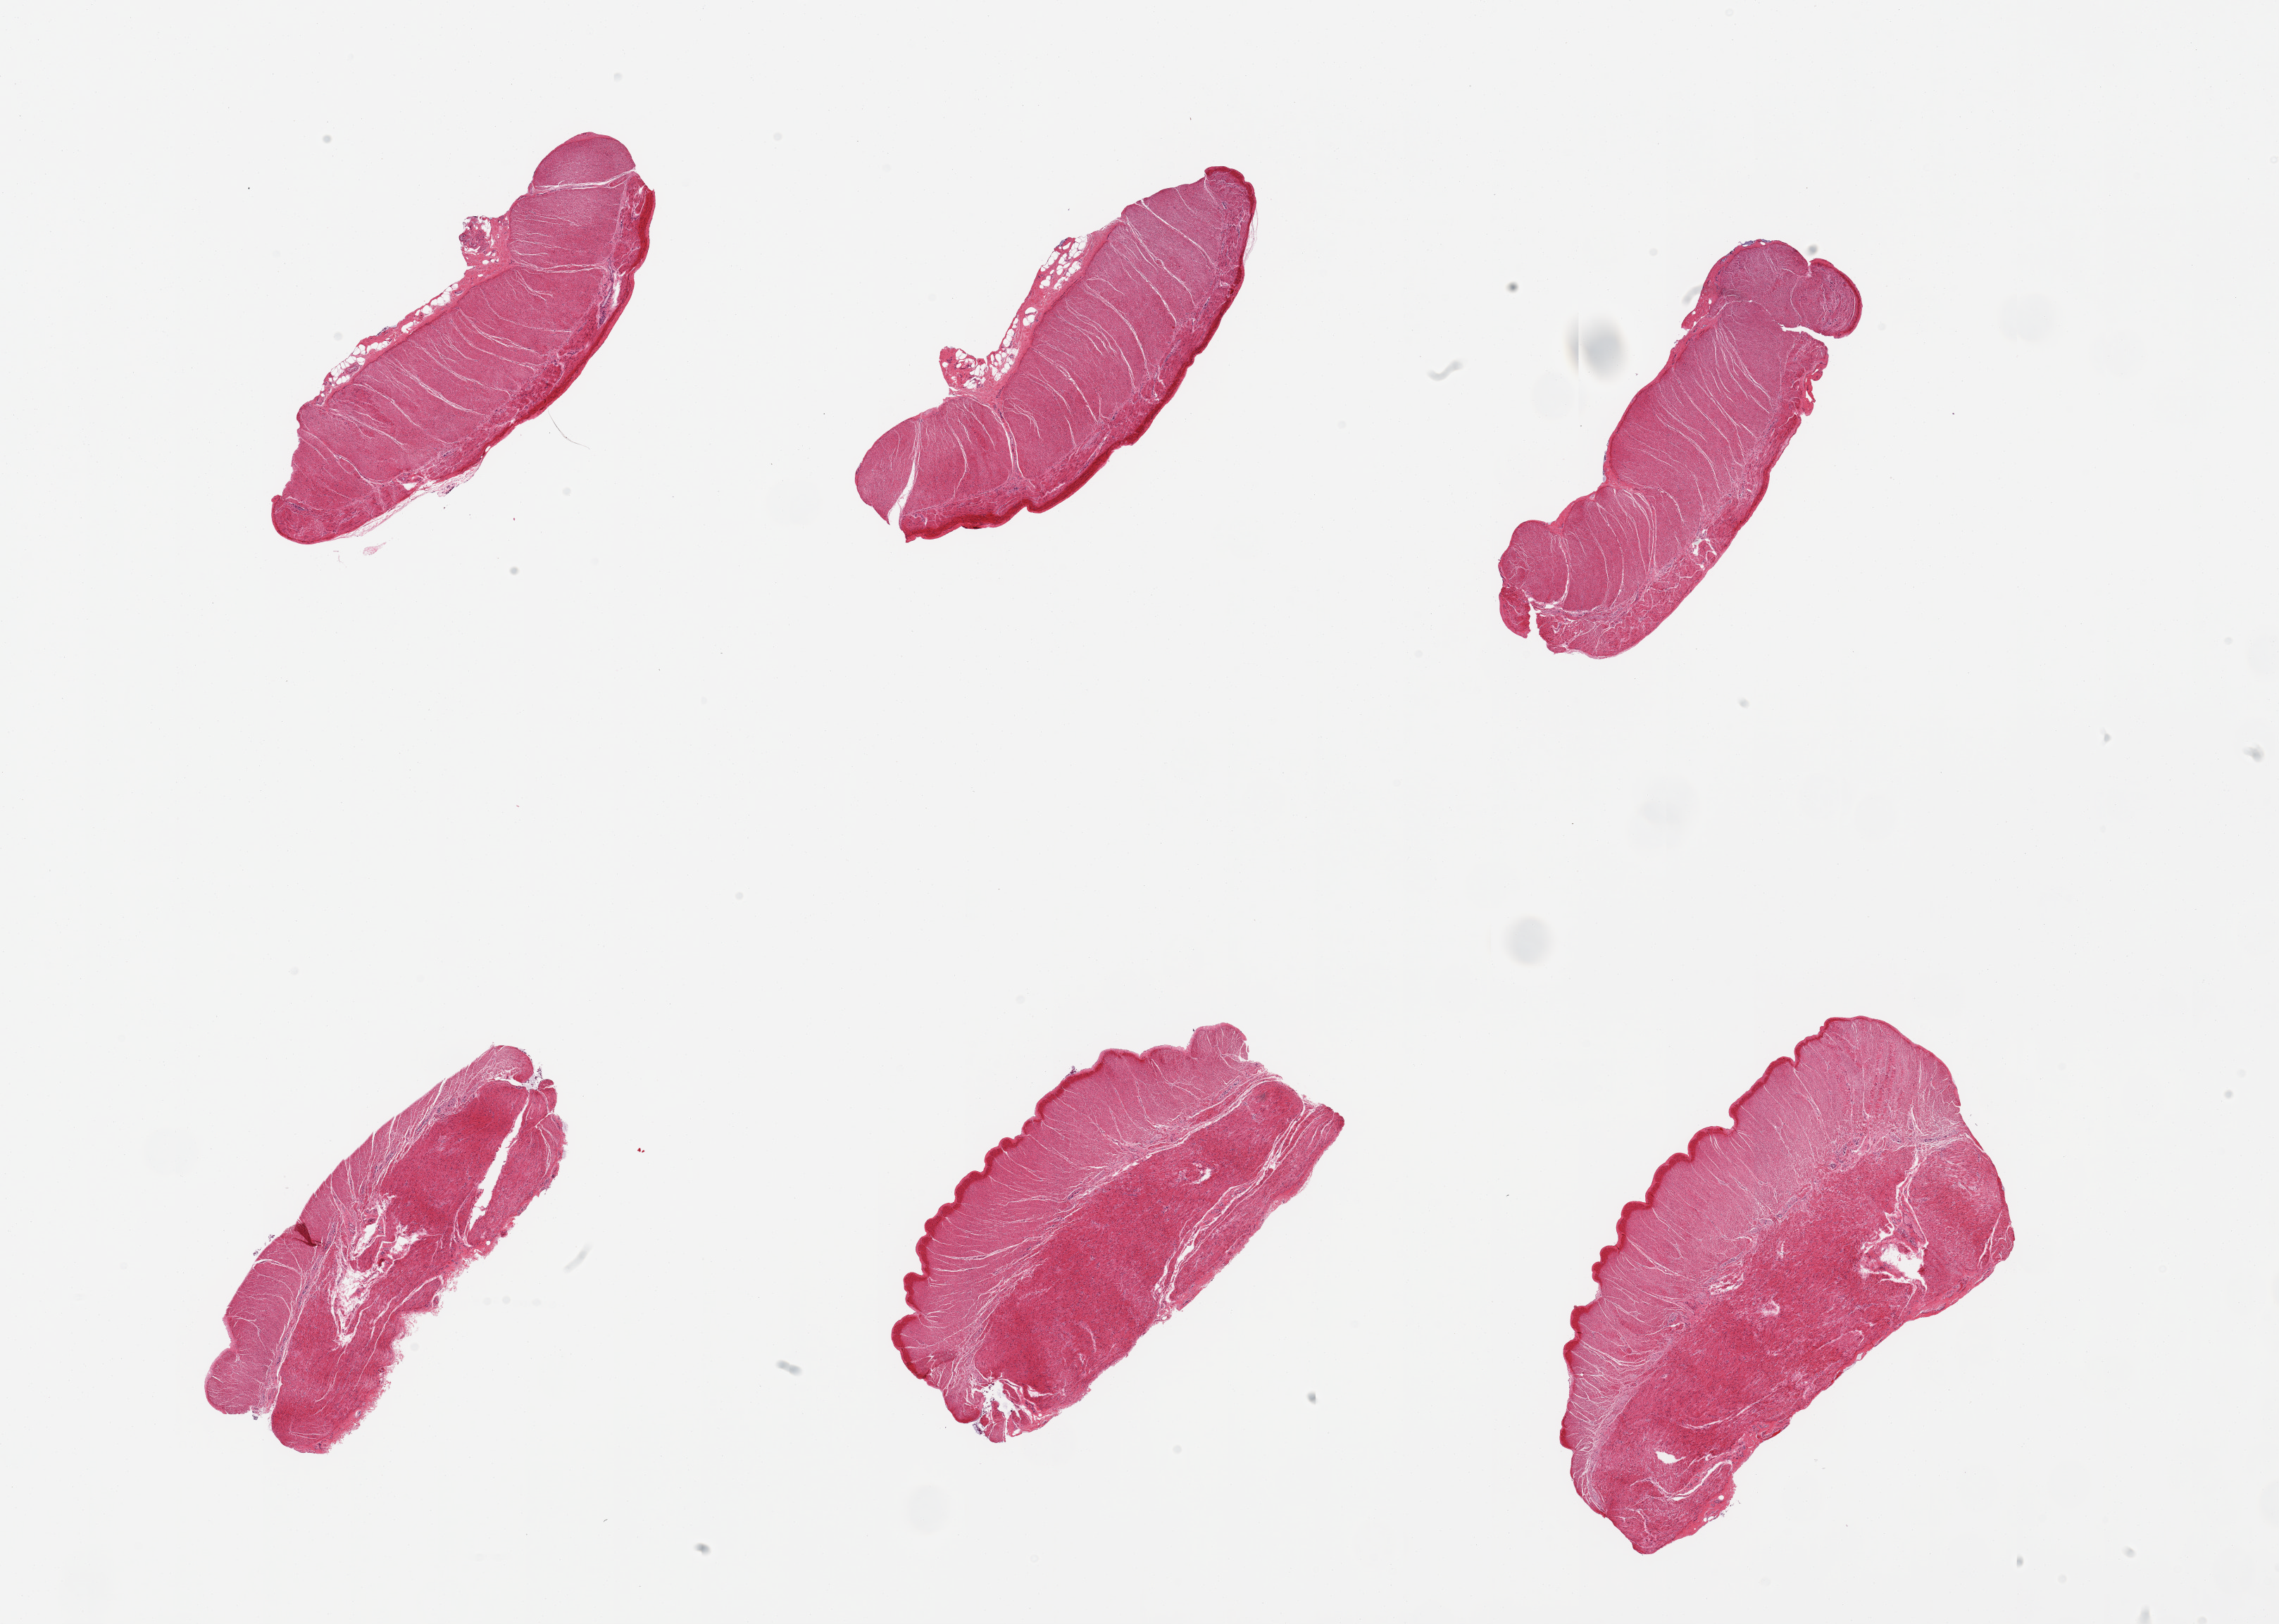
Digitized haematoxylin and eosin-stained section, brightfield — a low-resolution overview of the entire scanned area, about 25.6 x 18.2 mm; PAXgene-fixed paraffin-embedded (PFPE) section; target tissue: sigmoid colon; tissue donor sample. Donor sex: male.
- reviewer comment on this tissue sample: 6 pieces; well dissected muscularis